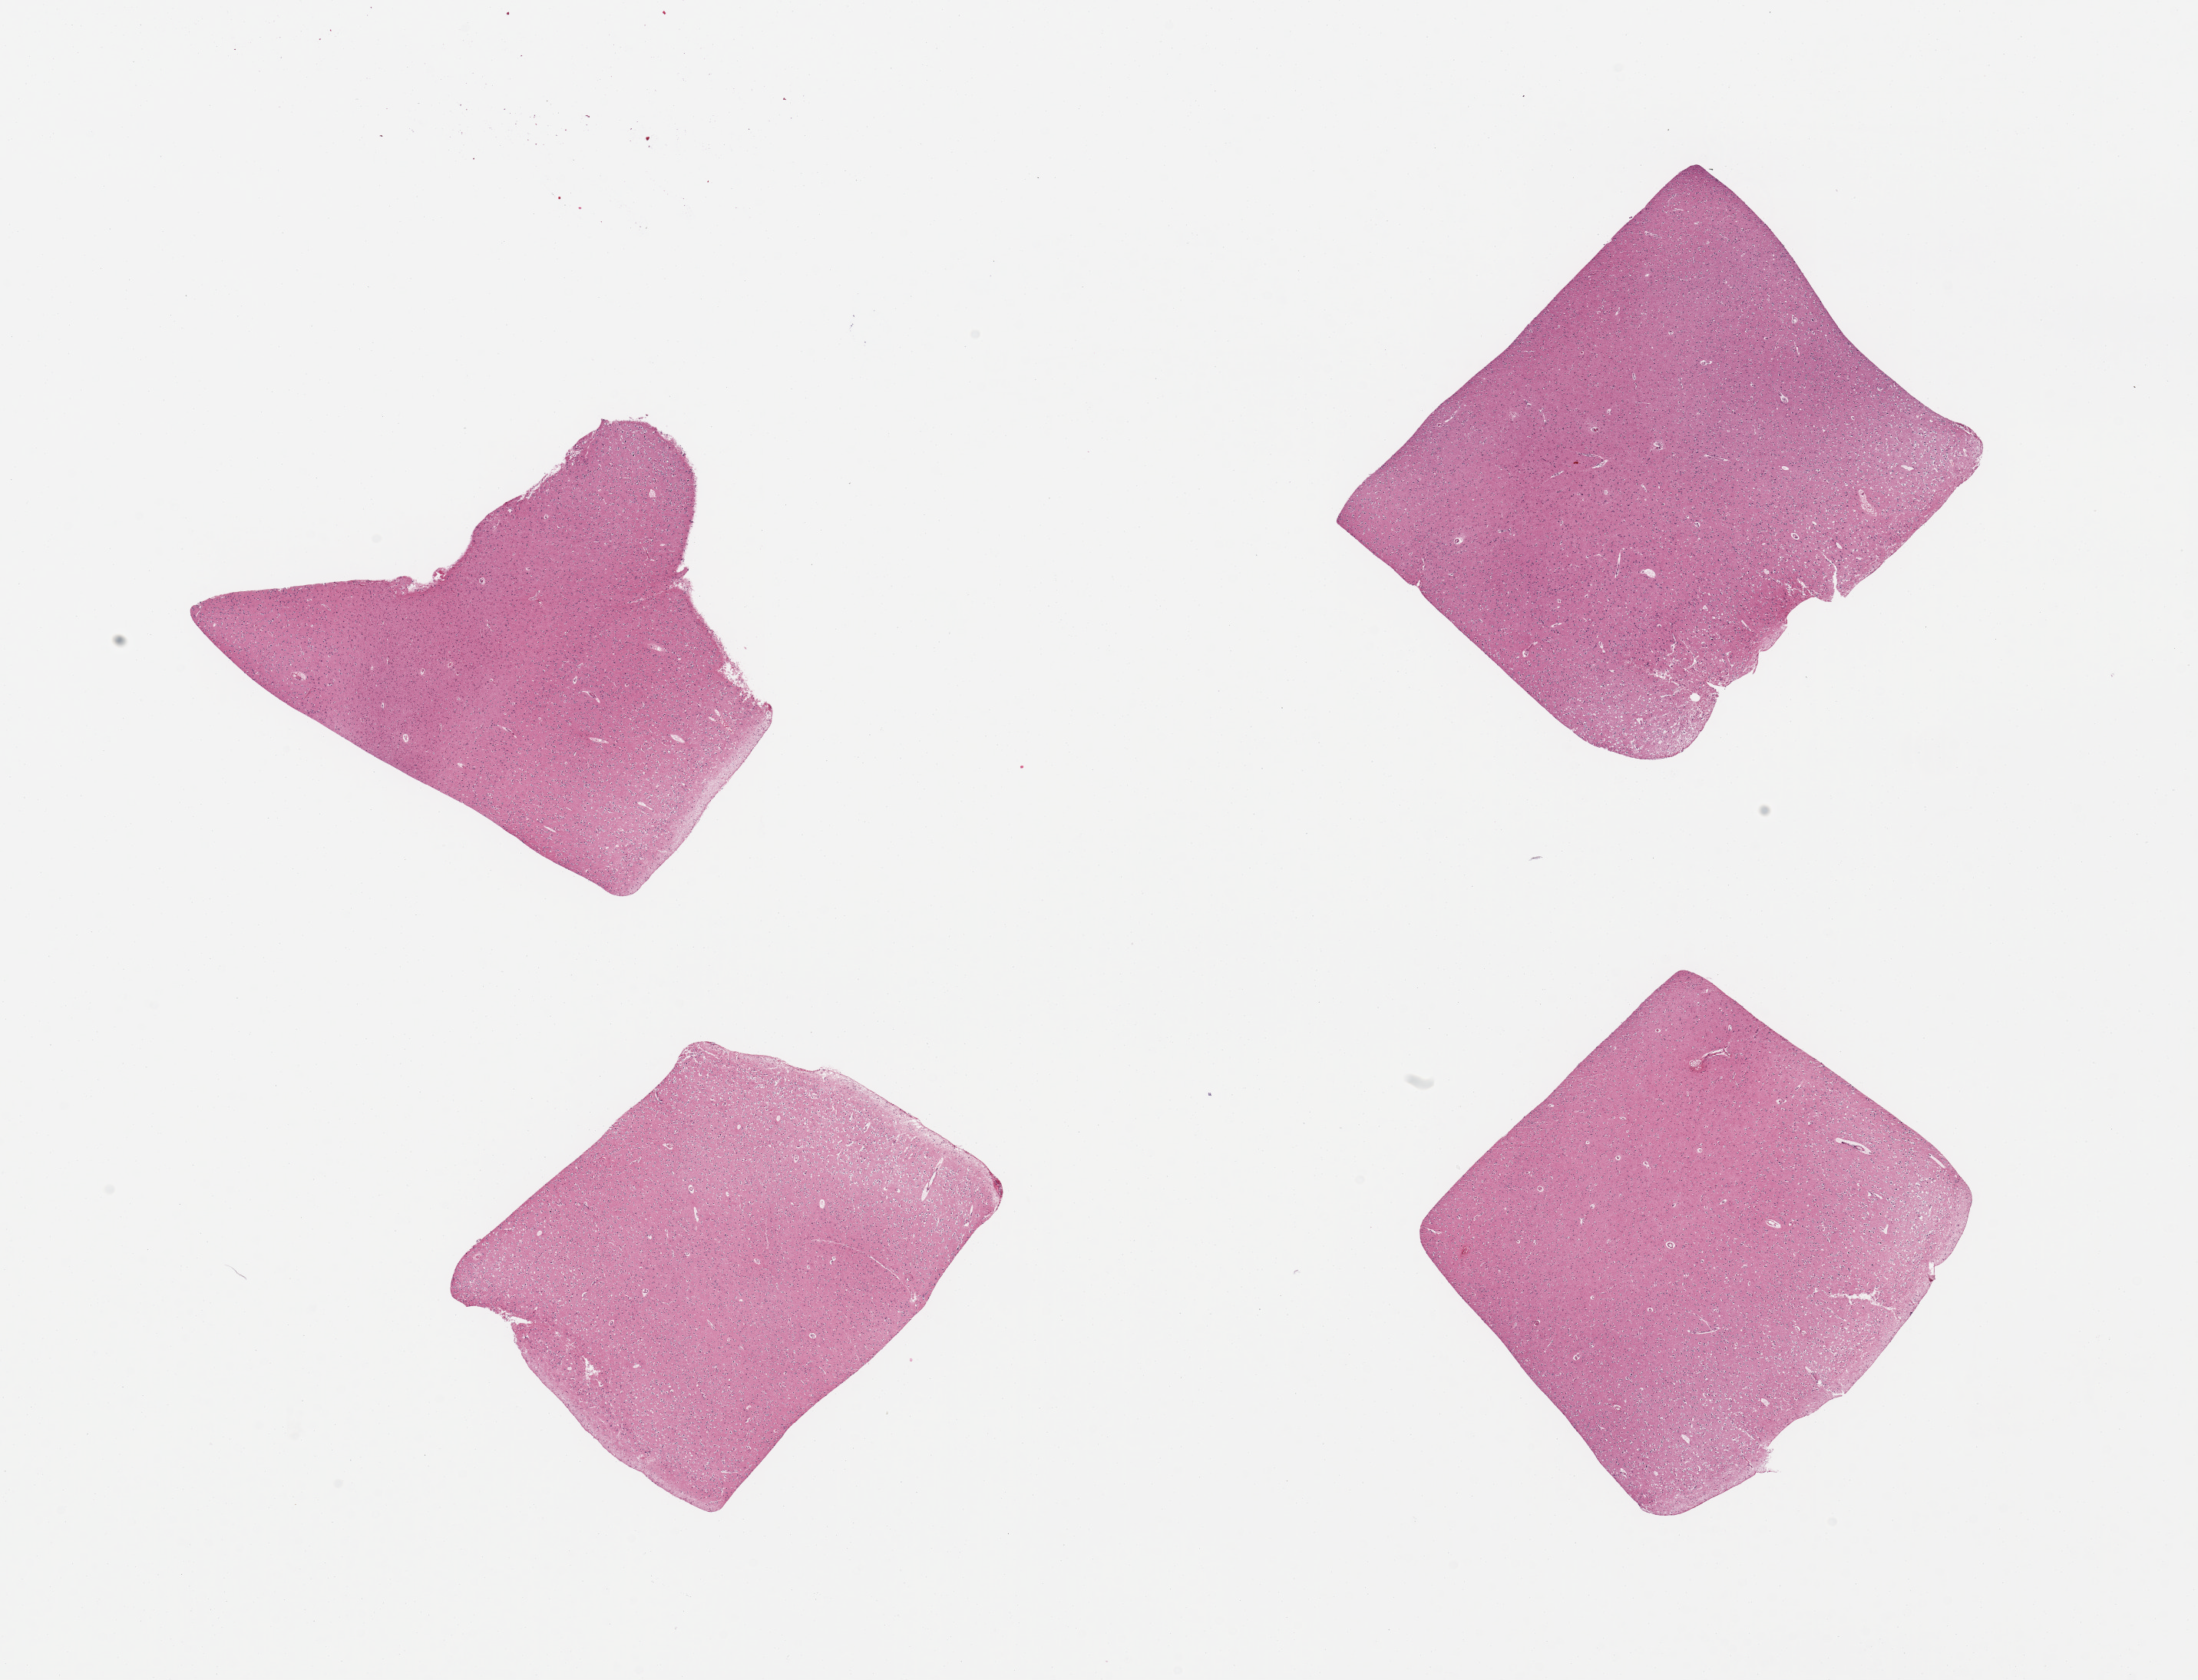
Hematoxylin and eosin (H&E) whole-slide image — shown as a low-resolution overview of the whole scanned area (about 22.6 x 17.3 mm, from a 20x scan), PAXgene-fixed paraffin-embedded (PFPE) section, section of cerebral cortex (target tissue), donor tissue sample. Donor: female.
Pathologist's review note for this sample: 4 pieces, no abnormalities.